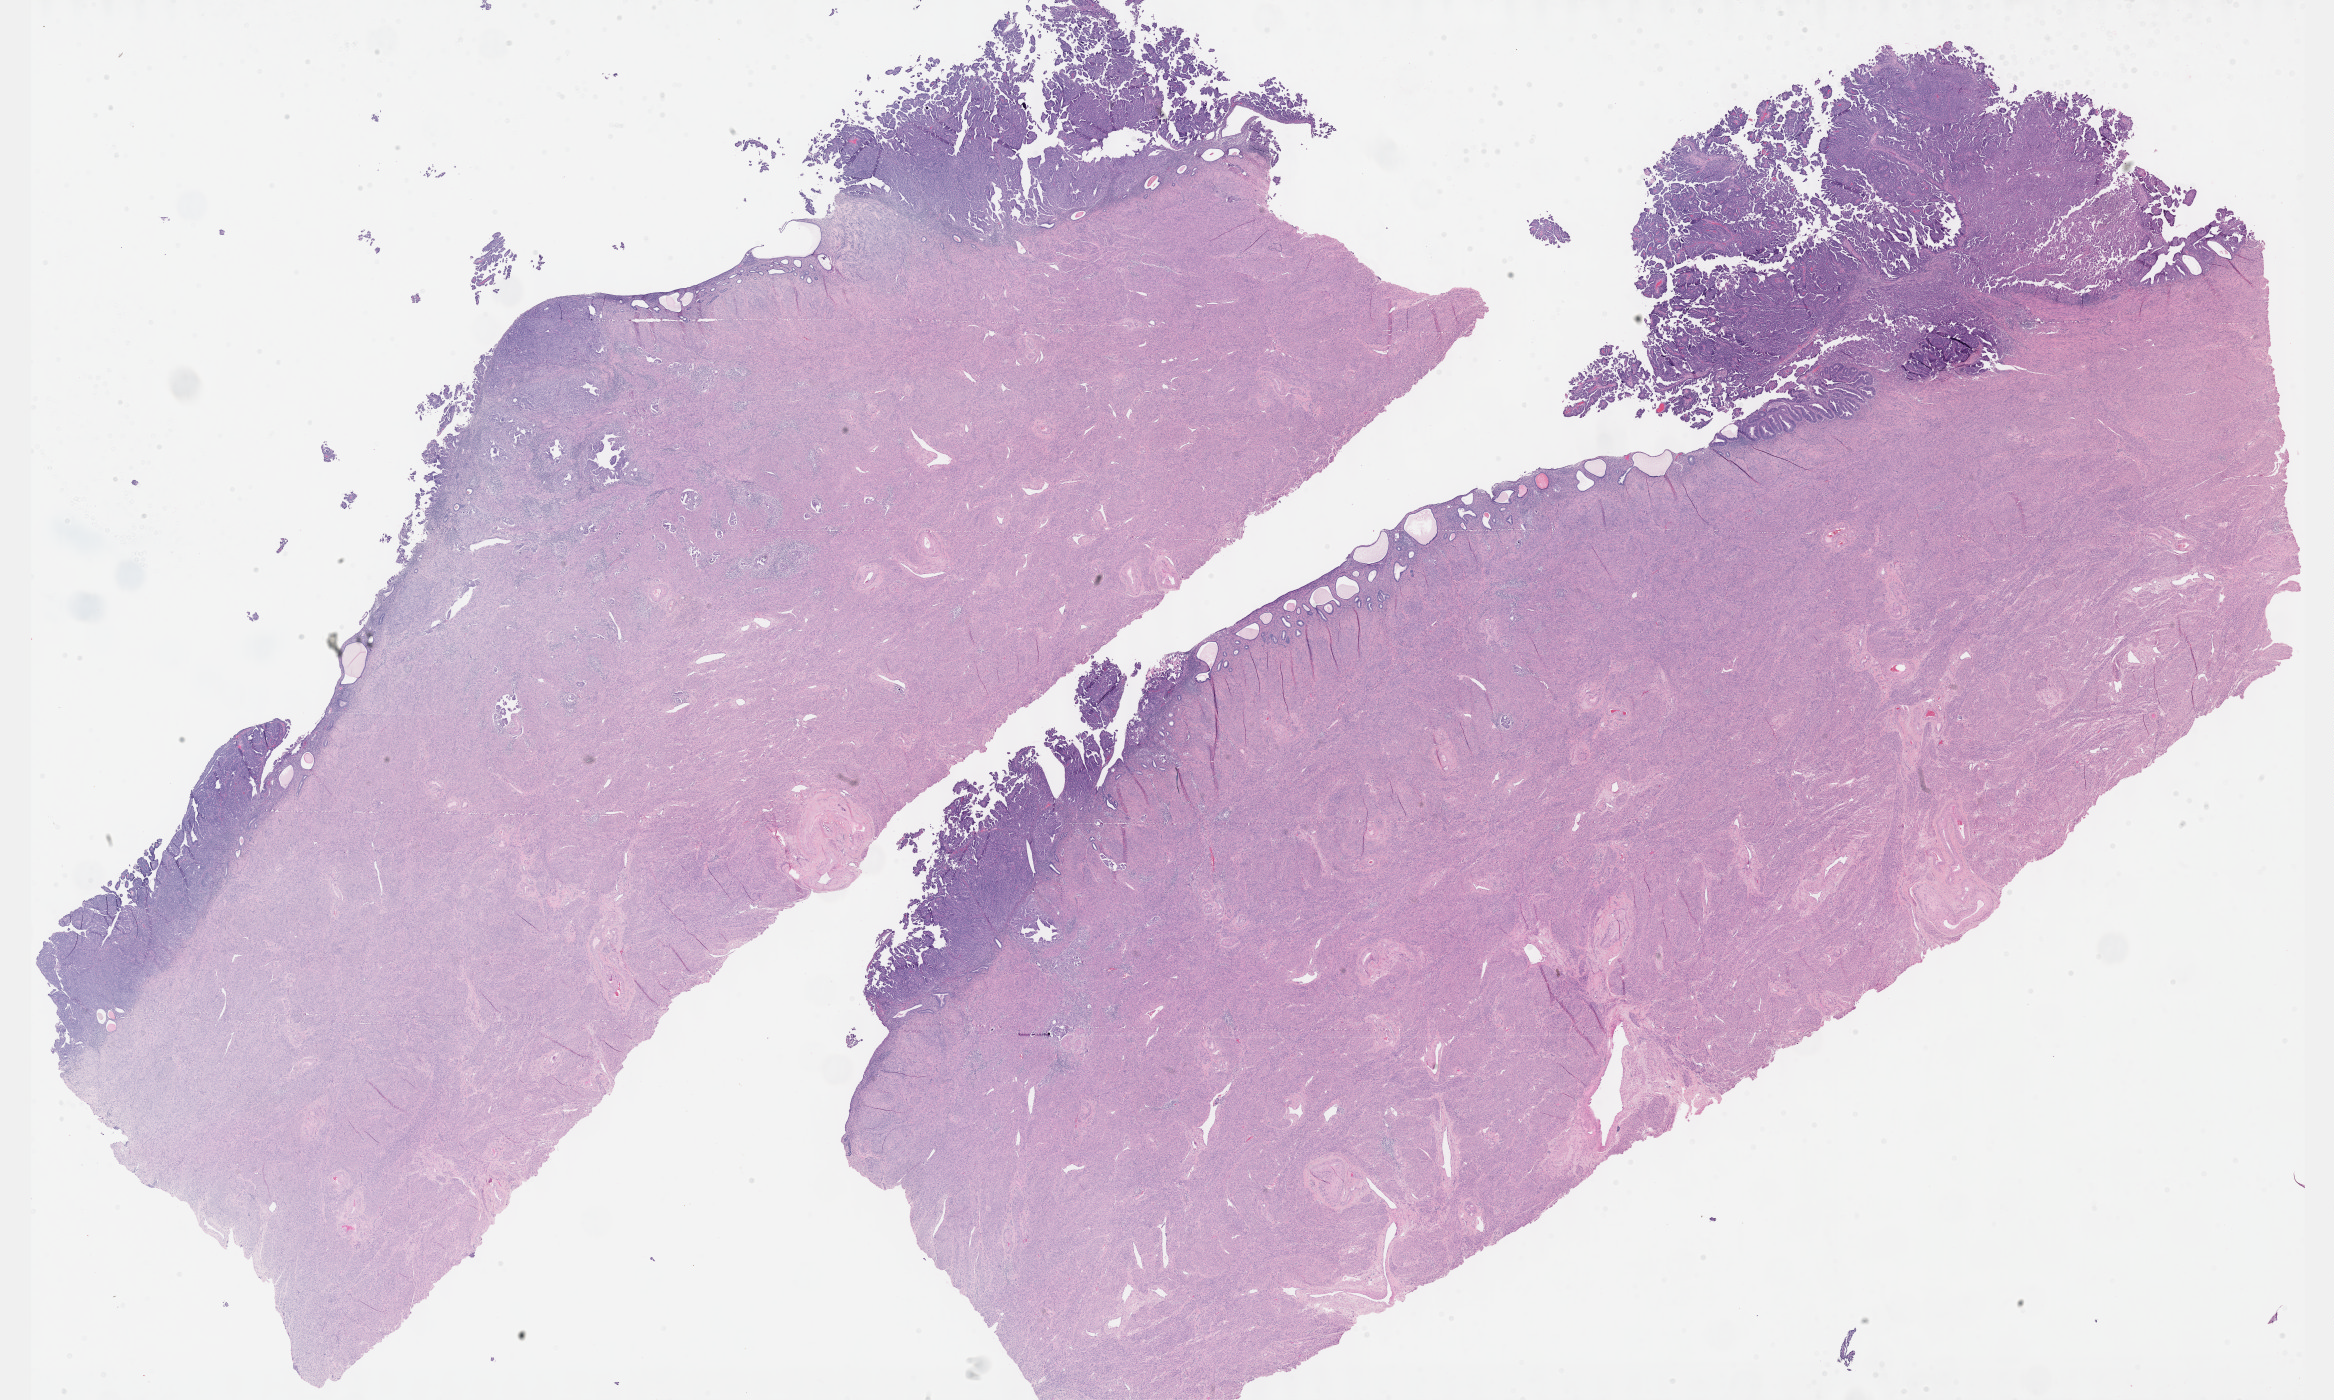
Digitized Hematoxylin and eosin (H&E) stained tissue section (whole slide), whole scanned area (about 37.7 x 22.6 mm) shown as a low-resolution overview. Formalin-fixed paraffin-embedded (FFPE) diagnostic section. Primary tumour sample from the uterus. Female patient; age at initial diagnosis 73 years. Histologic grade: G3 (poorly differentiated).
FIGO stage: IA. Histologic diagnosis: Serous surface papillary carcinoma (endometrium).